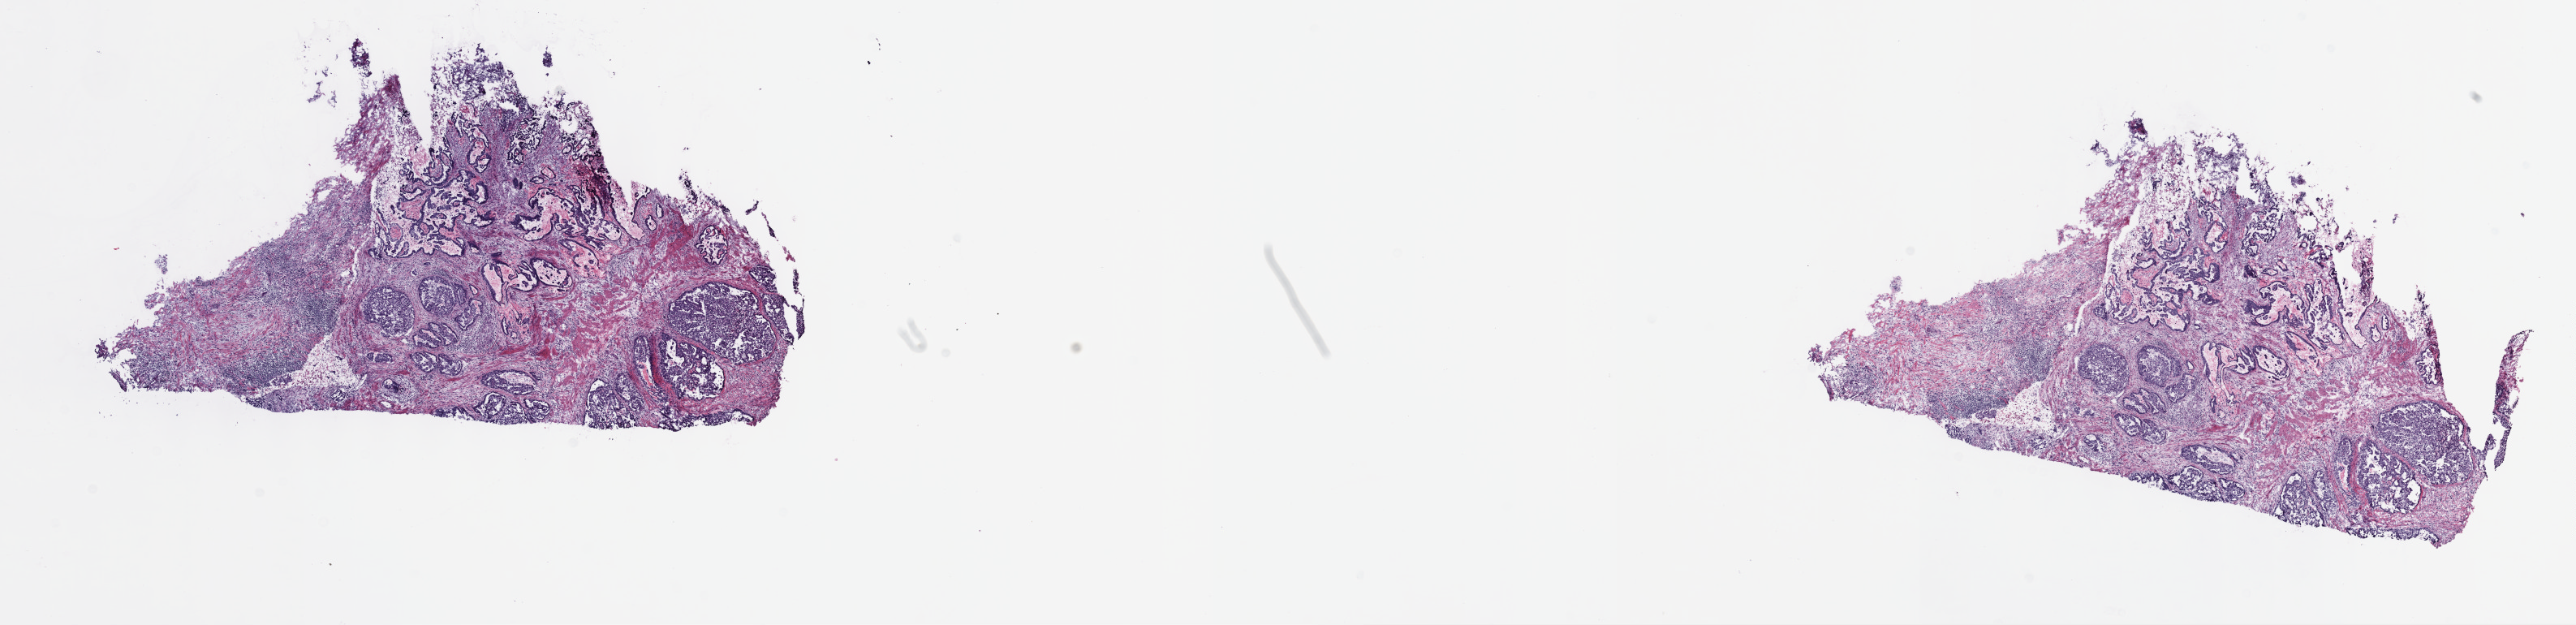
Whole-slide histology image, Hematoxylin and eosin (H&E) stained — whole scanned area (about 25.7 x 6.2 mm) shown as a low-resolution overview, frozen section from the top of the tissue portion, sample: primary tumour, stomach. Male, age 49 years at initial diagnosis. Pathologist review of this section (percent, as recorded): tumour cells 60%, tumour nuclei 60%.
Pathologic diagnosis: Papillary adenocarcinoma, NOS.